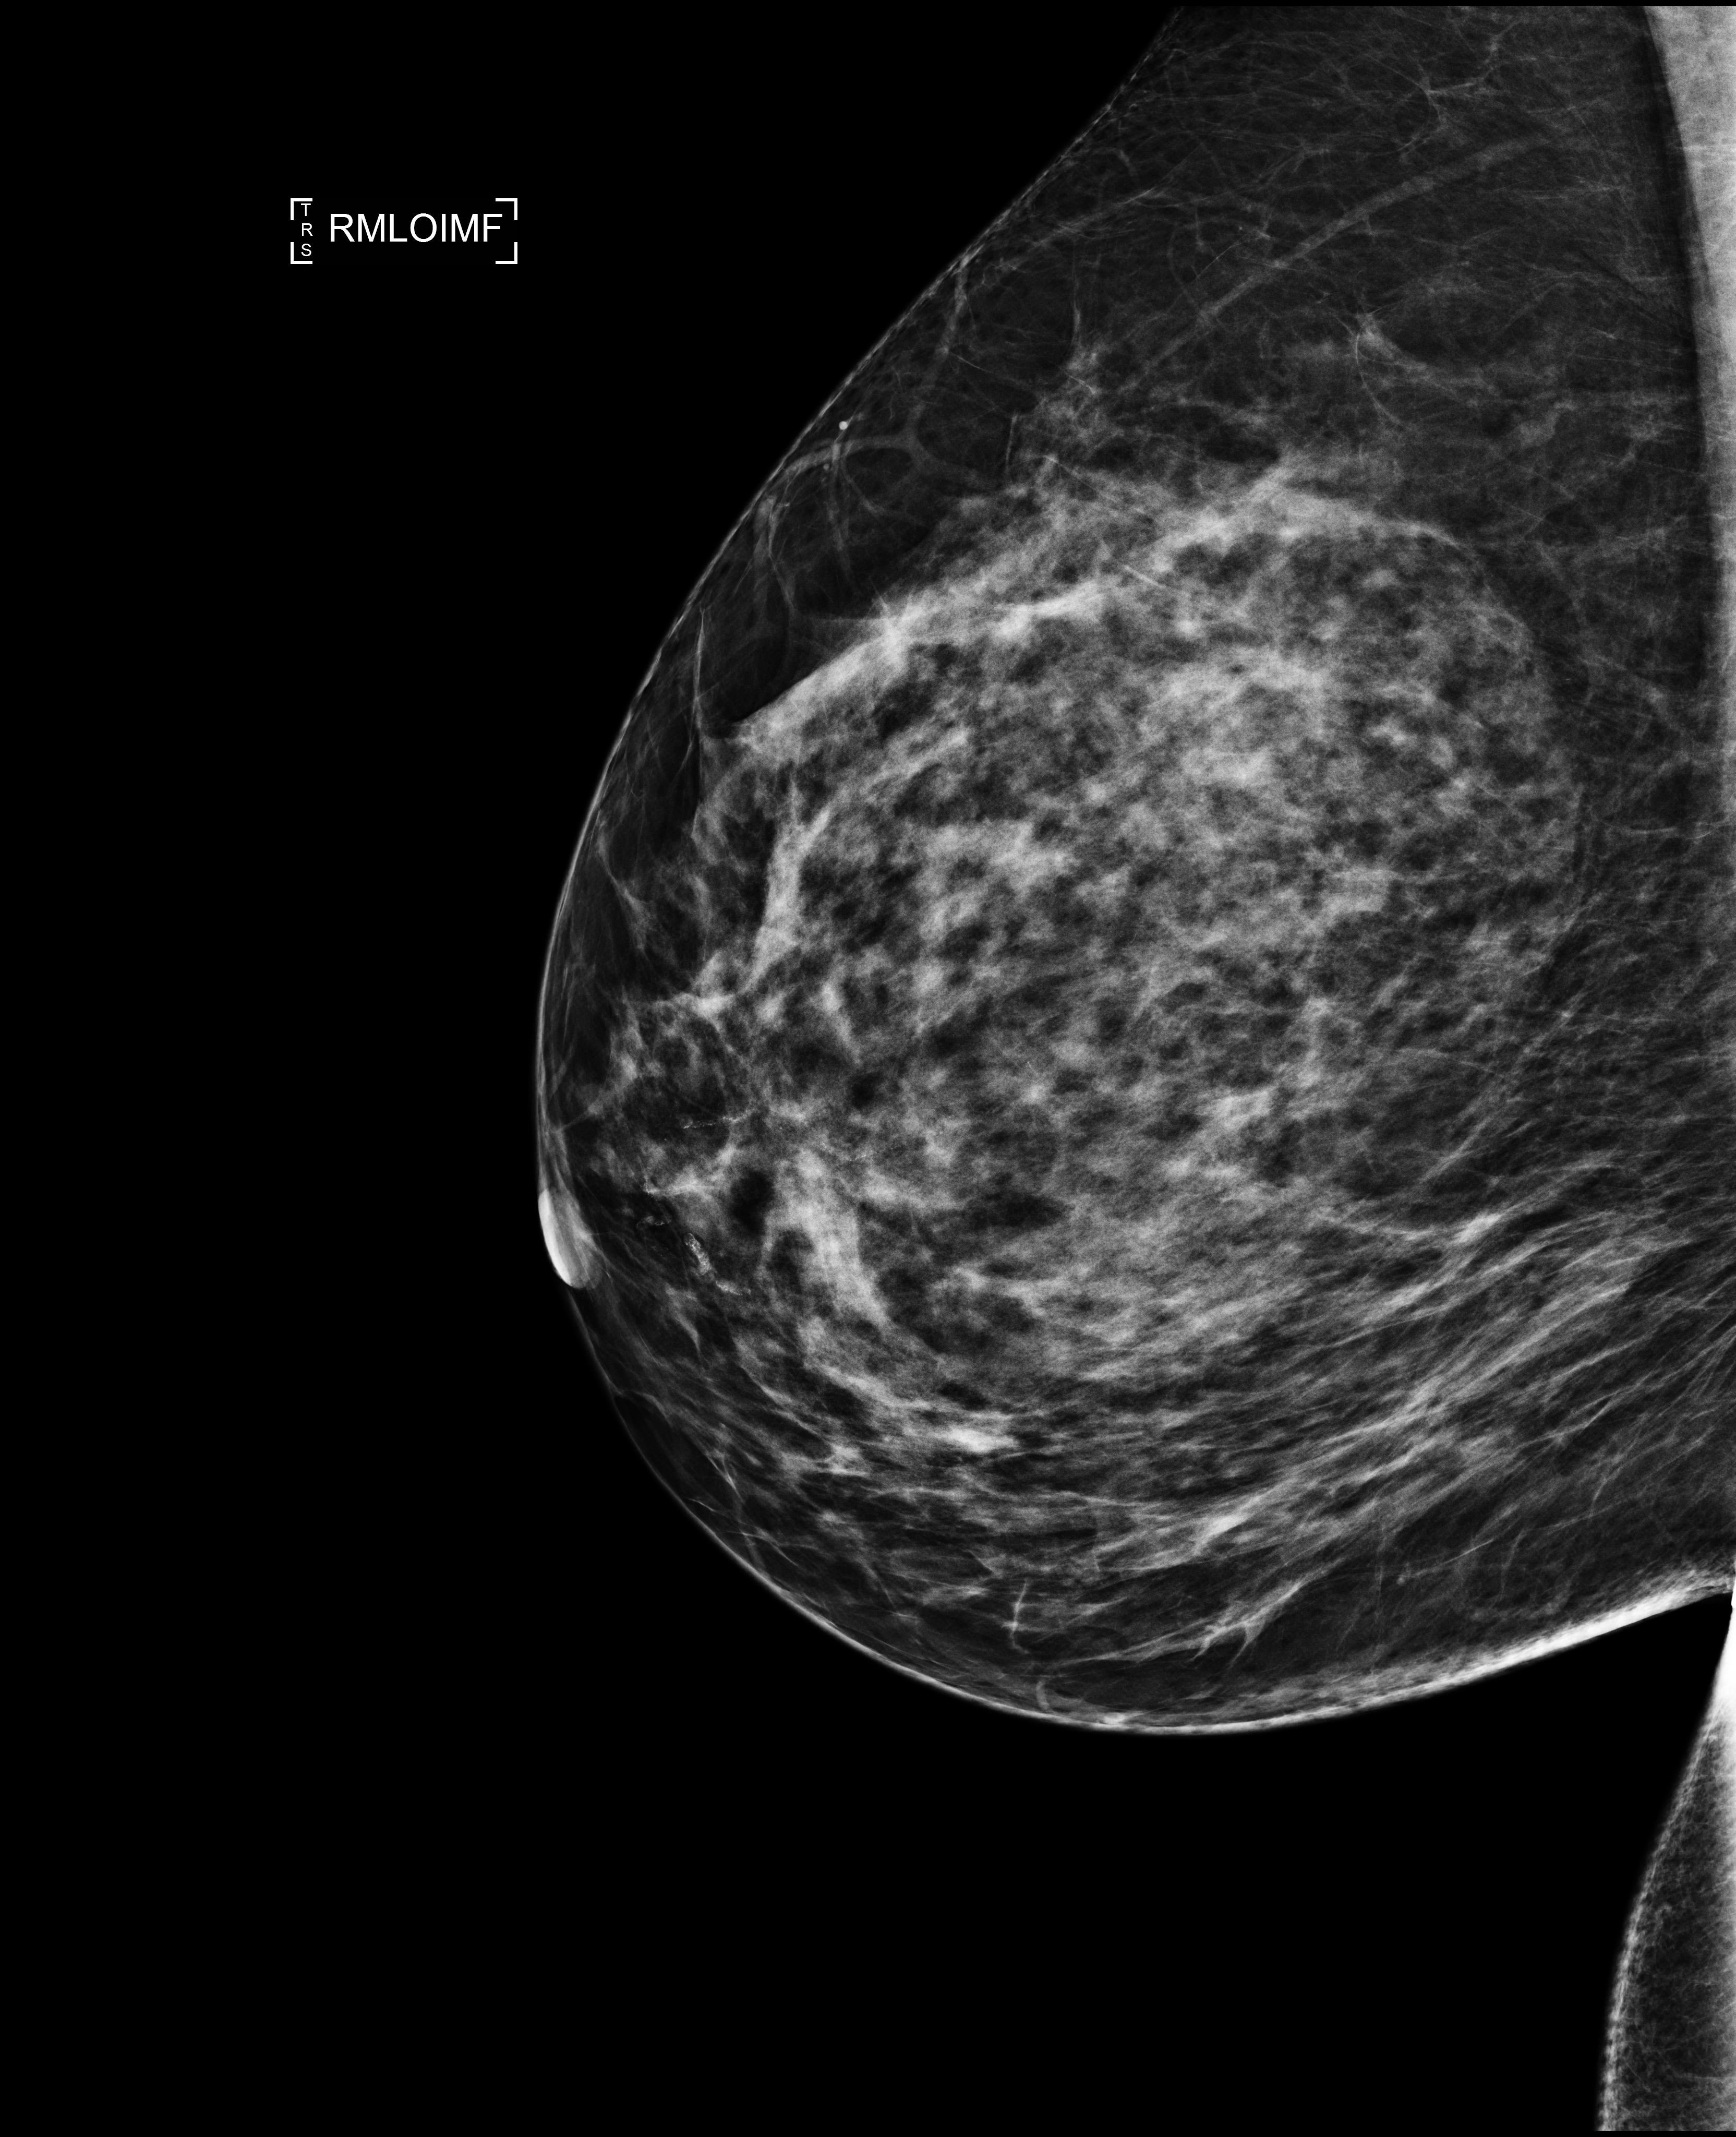
Screening examination, system: Selenia Dimensions. Female patient, age 45 years.
Image type: full-field digital mammogram. Breast: right. Projection: MLO view, infra-mammary fold.